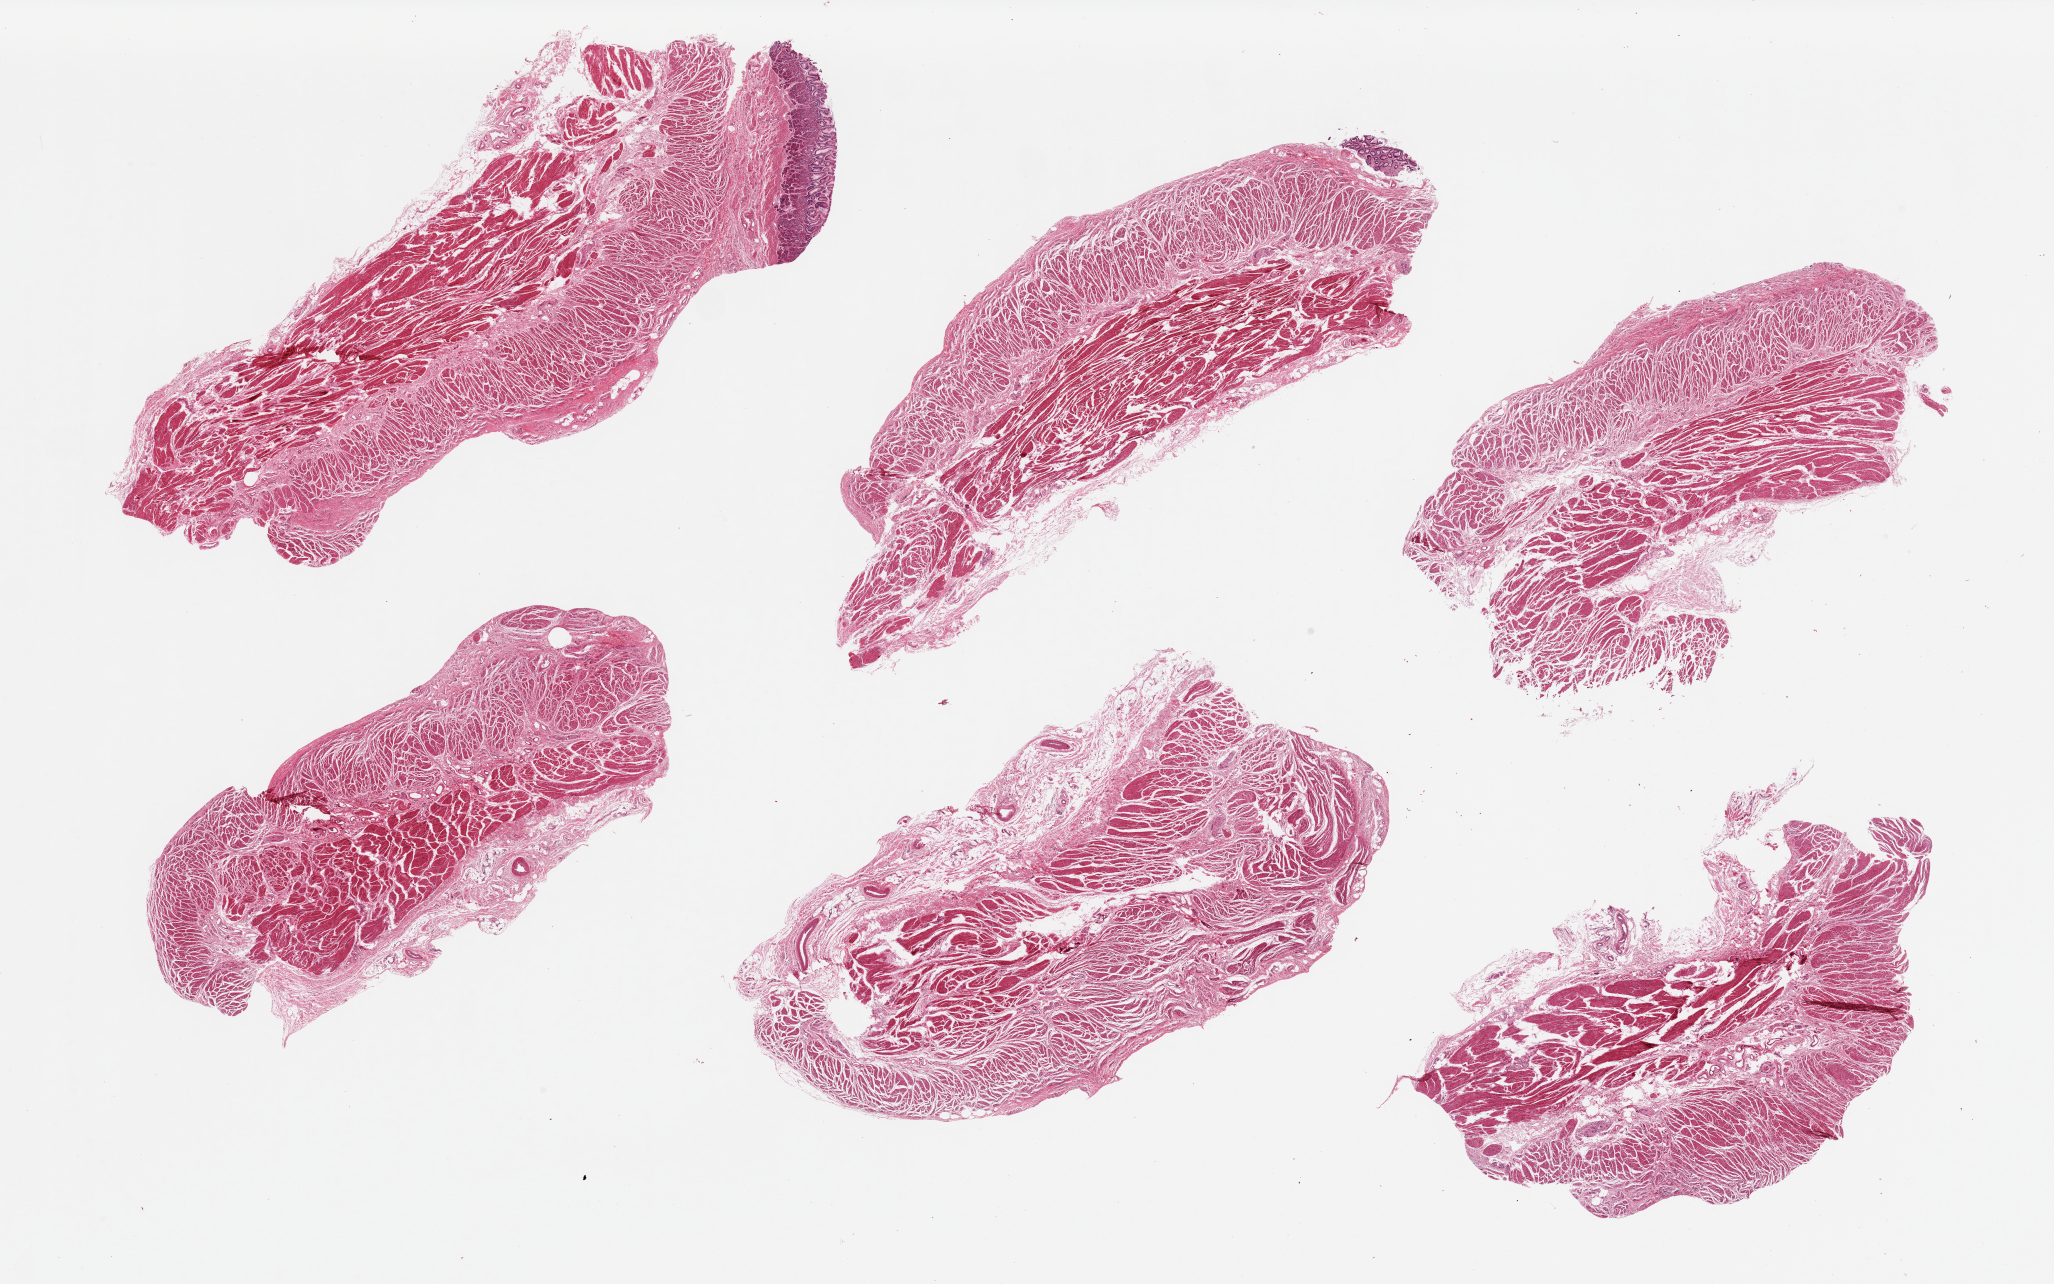
H&E whole-slide image, whole scanned area (about 32.5 x 20.3 mm) shown as a low-resolution overview. PAXgene-fixed, paraffin-embedded tissue. Target tissue: gastroesophageal junction. Tissue donor sample. Donor sex: female.
Review note (as recorded): 6 pieces, 2 with residual mucosa (not target).